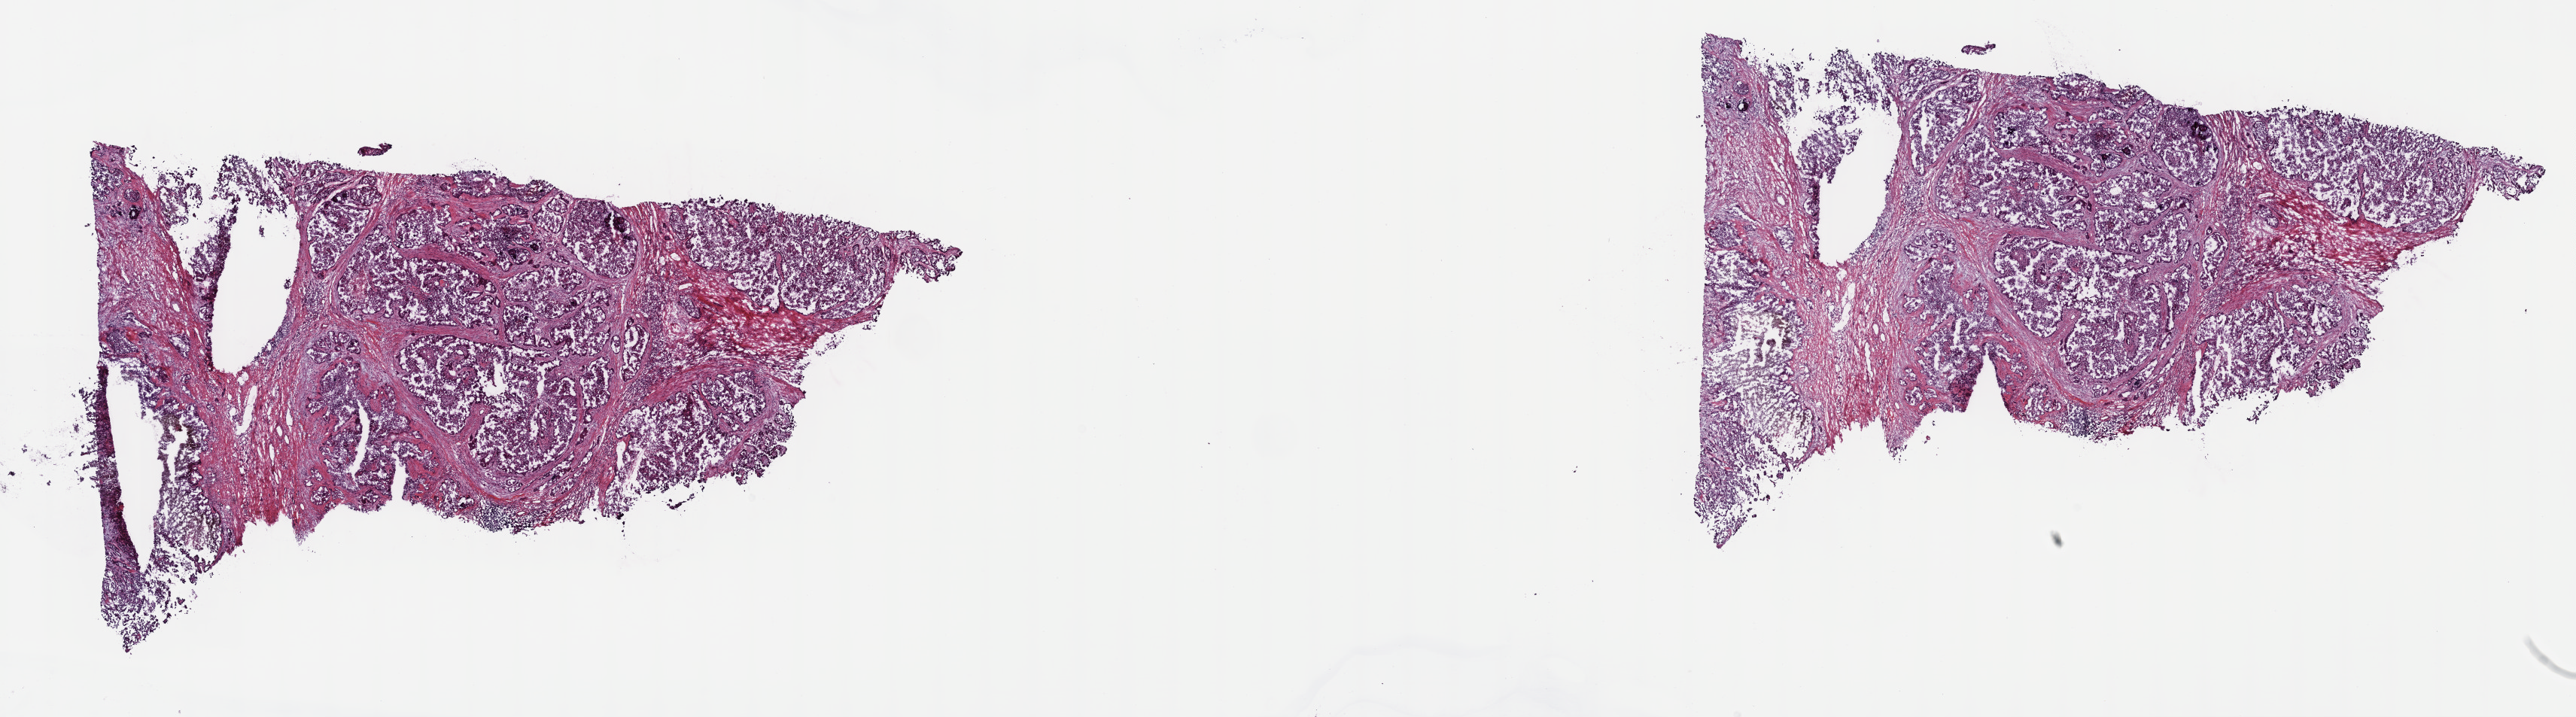
Digitized H&E-stained tissue section (whole slide) — low-resolution overview of the scanned area, about 27.7 x 7.7 mm; frozen section from the top of the tissue portion; primary tumour sample from the kidney. Patient: male, age at initial diagnosis 54 years. Composition of this section per pathologist review: tumour cells 100%, tumour nuclei 60%, normal cells 0%, stromal cells 0%, necrosis 0%. Infiltration values recorded for this section: lymphocyte infiltration 2%, monocyte infiltration 2%, neutrophil infiltration 0%.
Pathologic diagnosis: Papillary adenocarcinoma, NOS. AJCC pathologic stage: III (6th edition). Laterality: left.